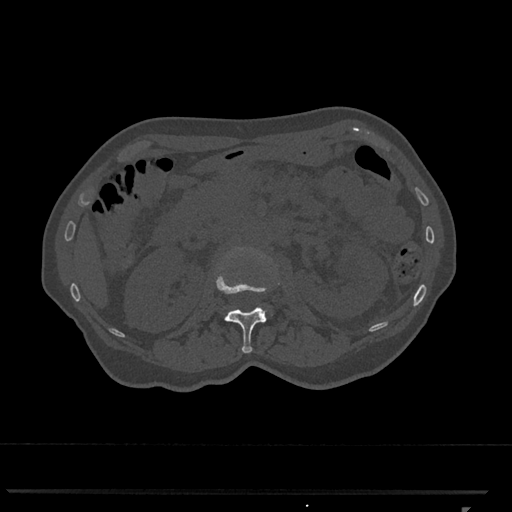
CT including the spine, one axial slice. Slice 384 of 793 in the series (ordered by position). Reconstruction kernel Br40s/3. 120 kVp. Bone window (W 1800 / L 400 HU). 0.5 mm slice thickness. 512 × 512 image matrix, field of view 380 × 380 mm. Female patient, age 62 years. From the clinical record (not read from this slice): primary cancer: renal.
Structures marked on this image (semi-automatically segmented with operator editing):
- L1 vertebra: bounding box (x1, y1, x2, y2) in pixels: (216, 249, 280, 353)
- L2 vertebra: (259, 253, 261, 255)